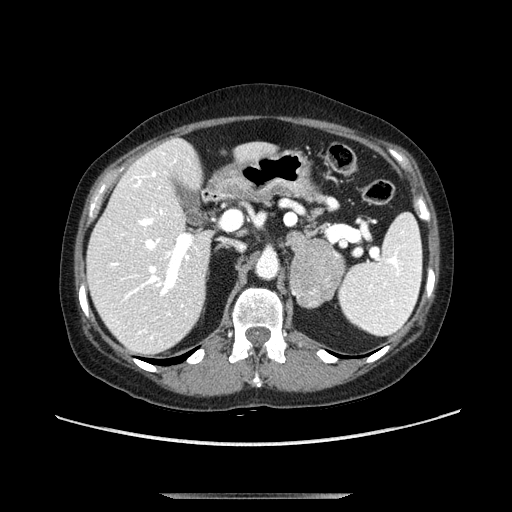
Contrast-enhanced abdominal CT, one axial slice; slice 66 of 107 in the series (ordered by position); soft-tissue window (W 400 / L 40 HU); 512 × 512 image matrix, field of view 380 × 380 mm. Female patient. Case-level facts recorded for this patient, not image findings: diagnosis: adrenocortical carcinoma; tumour side: left adrenal; tumour size at pathology: 7.5 cm; Ki-67 index: 9 %; stage (as recorded): 3.
Annotated regions visible in this slice (semi-automatic segmentation, software-assisted and operator-edited):
- mass: box from (x=289, y=238) to (x=345, y=308) px